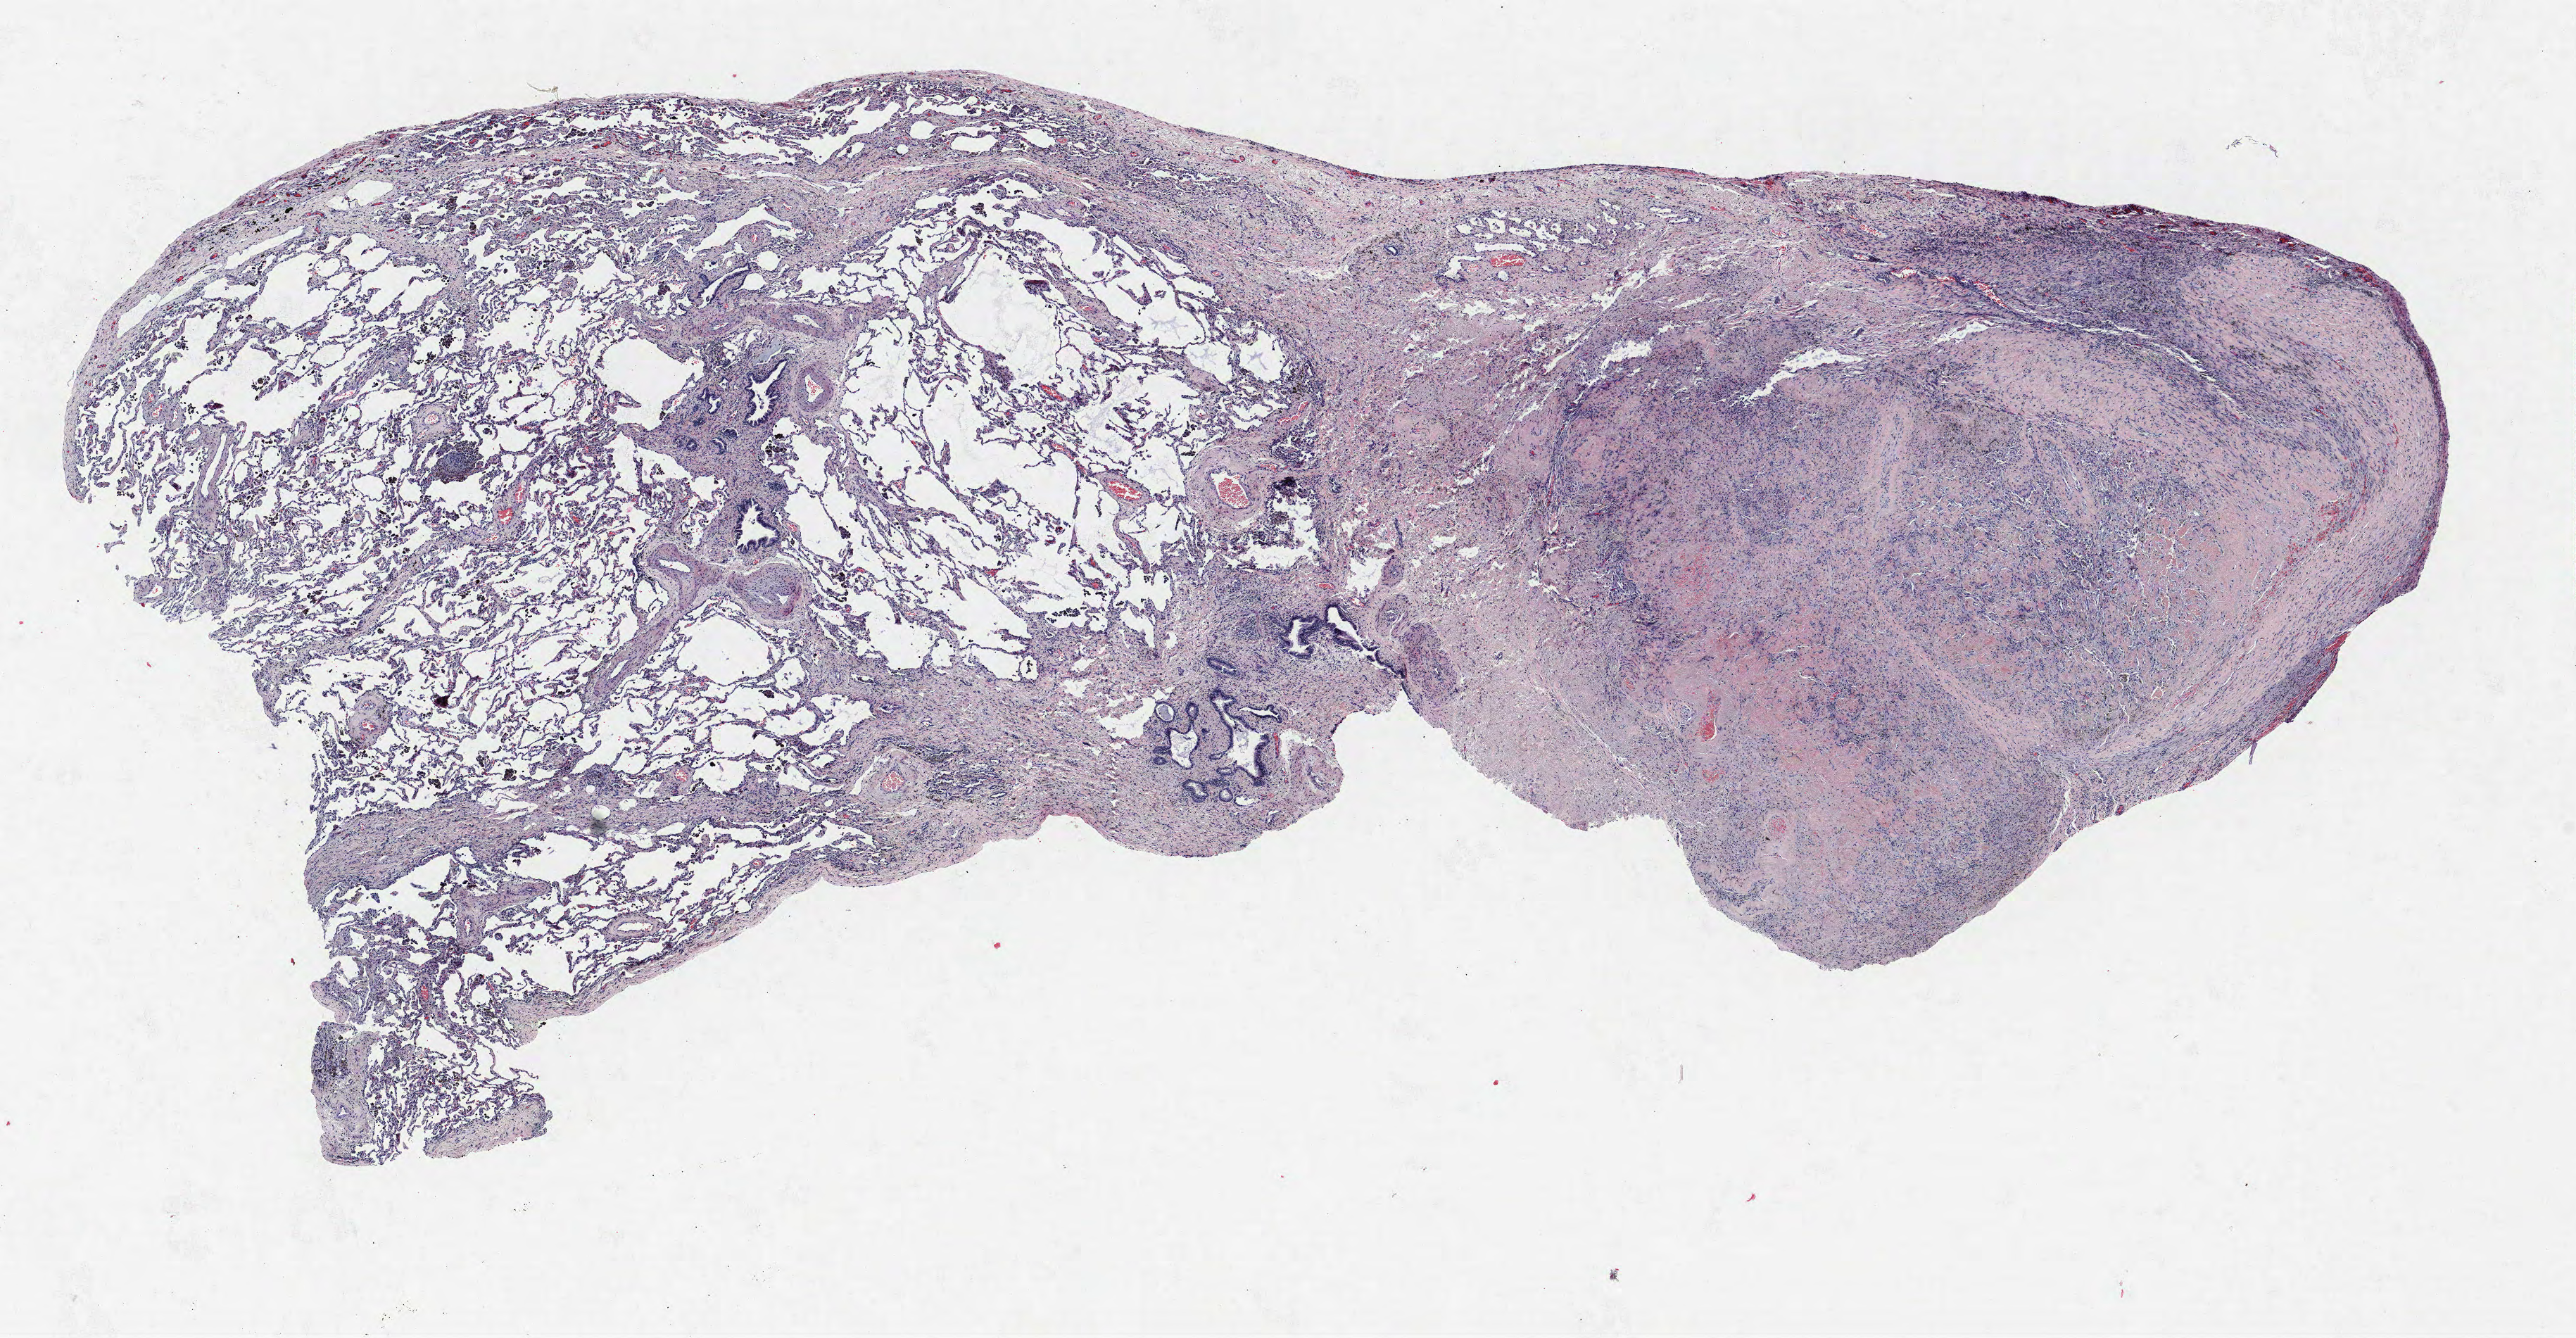
Whole-slide histology image, H&E-stained — low-resolution overview of the scanned area, about 14.6 x 7.6 mm (from a 40x scan), FFPE section, lung tissue. Male, age 64 at enrolment. Grade: well differentiated (G1).
Stage (AJCC 6th edition): IB. Participant's lung-cancer diagnosis: Adenocarcinoma, NOS. Tumour size (pathology): 45 mm. Primary tumour location (clinical record): right upper lobe.